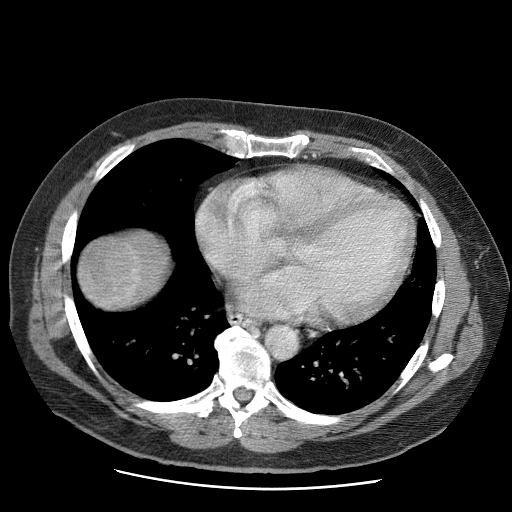
Contrast-enhanced abdominal CT (liver protocol), one axial slice; position 67 of 81 along the scan axis; soft-tissue window (W 400 / L 40 HU); 2.5 mm slice thickness; 512 × 512 image matrix, field of view 380 × 380 mm. From the clinical record (not read from this slice): diagnosis: hepatocellular carcinoma (patient treated with transarterial chemoembolisation; whether this scan precedes or follows treatment is not stated here); TNM stage (as recorded): Stage-IIIA; Child-Pugh class: A; tumour size: 5.5 cm.
Outlined on this slice (semi-automatically segmented with operator editing):
- liver parenchyma outside the tumour (the mass and vessels are separate outlines, so this box may not span the whole liver): box from (x=78, y=230) to (x=168, y=308) px
- mass: (x=78, y=238)–(x=143, y=309)